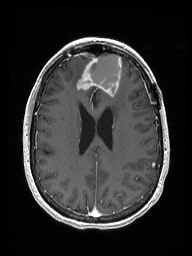
Brain MRI from a brain-tumour surgery series, one axial slice; position 65 of 192 along the scan axis; T1-weighted post-contrast; 192 × 256 image matrix, field of view 187 × 250 mm. Case-level facts recorded for this patient, not image findings: histopathology: Metastastic Carcinoma from Breast primary; tumour location: Right Frontal.
Annotated regions visible in this slice (manually delineated by an expert):
- previous resection cavity: bounding box <89,54,122,96> (left, top, right, bottom; pixels)